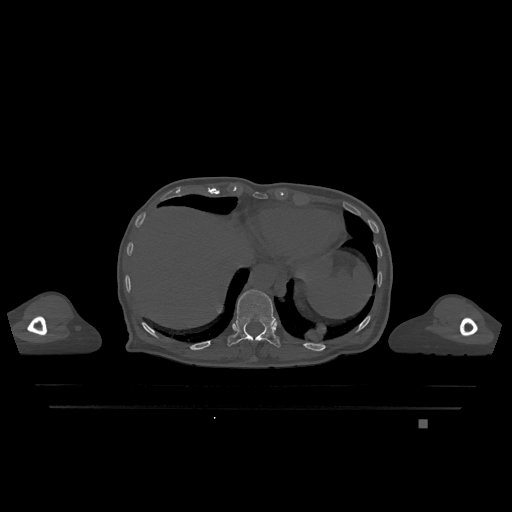
CT including the spine, one axial slice; position 596 of 1317 along the scan axis; bone window (W 1800 / L 400 HU); 0.5 mm slice thickness; 512 × 512 image matrix, field of view 500 × 500 mm. Patient: female, 74 years. From the clinical record (not read from this slice): primary cancer: lung; vertebrae with lytic lesions (as recorded): T1, T4, T5, T6, L4, L5.
Annotated regions visible in this slice (semi-automatic segmentation, software-assisted and operator-edited):
- T11 vertebra: bounding box [x1, y1, x2, y2] px = [227, 289, 281, 348]